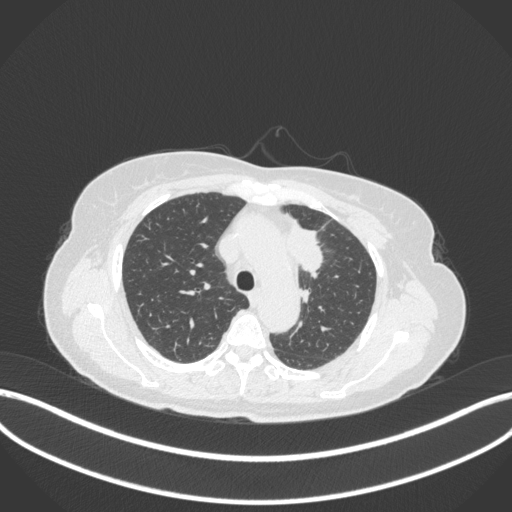
Chest CT, one axial slice. Position 242 of 368 along the scan axis. Reconstruction kernel B31f. 120 kVp. Lung window (W 1500 / L -600 HU). 512 × 512 image matrix, field of view 400 × 400 mm. Female patient, age 65 years. From the clinical record (not read from this slice): clinical TNM (as recorded): T2a N0 M0; histopathological grade: G2-3.
Outlined on this slice (rectangle marked by the reading radiologist):
- lung tumour (recorded histology: adenocarcinoma): bounding box (x1, y1, x2, y2) in pixels: (286, 219, 330, 276)